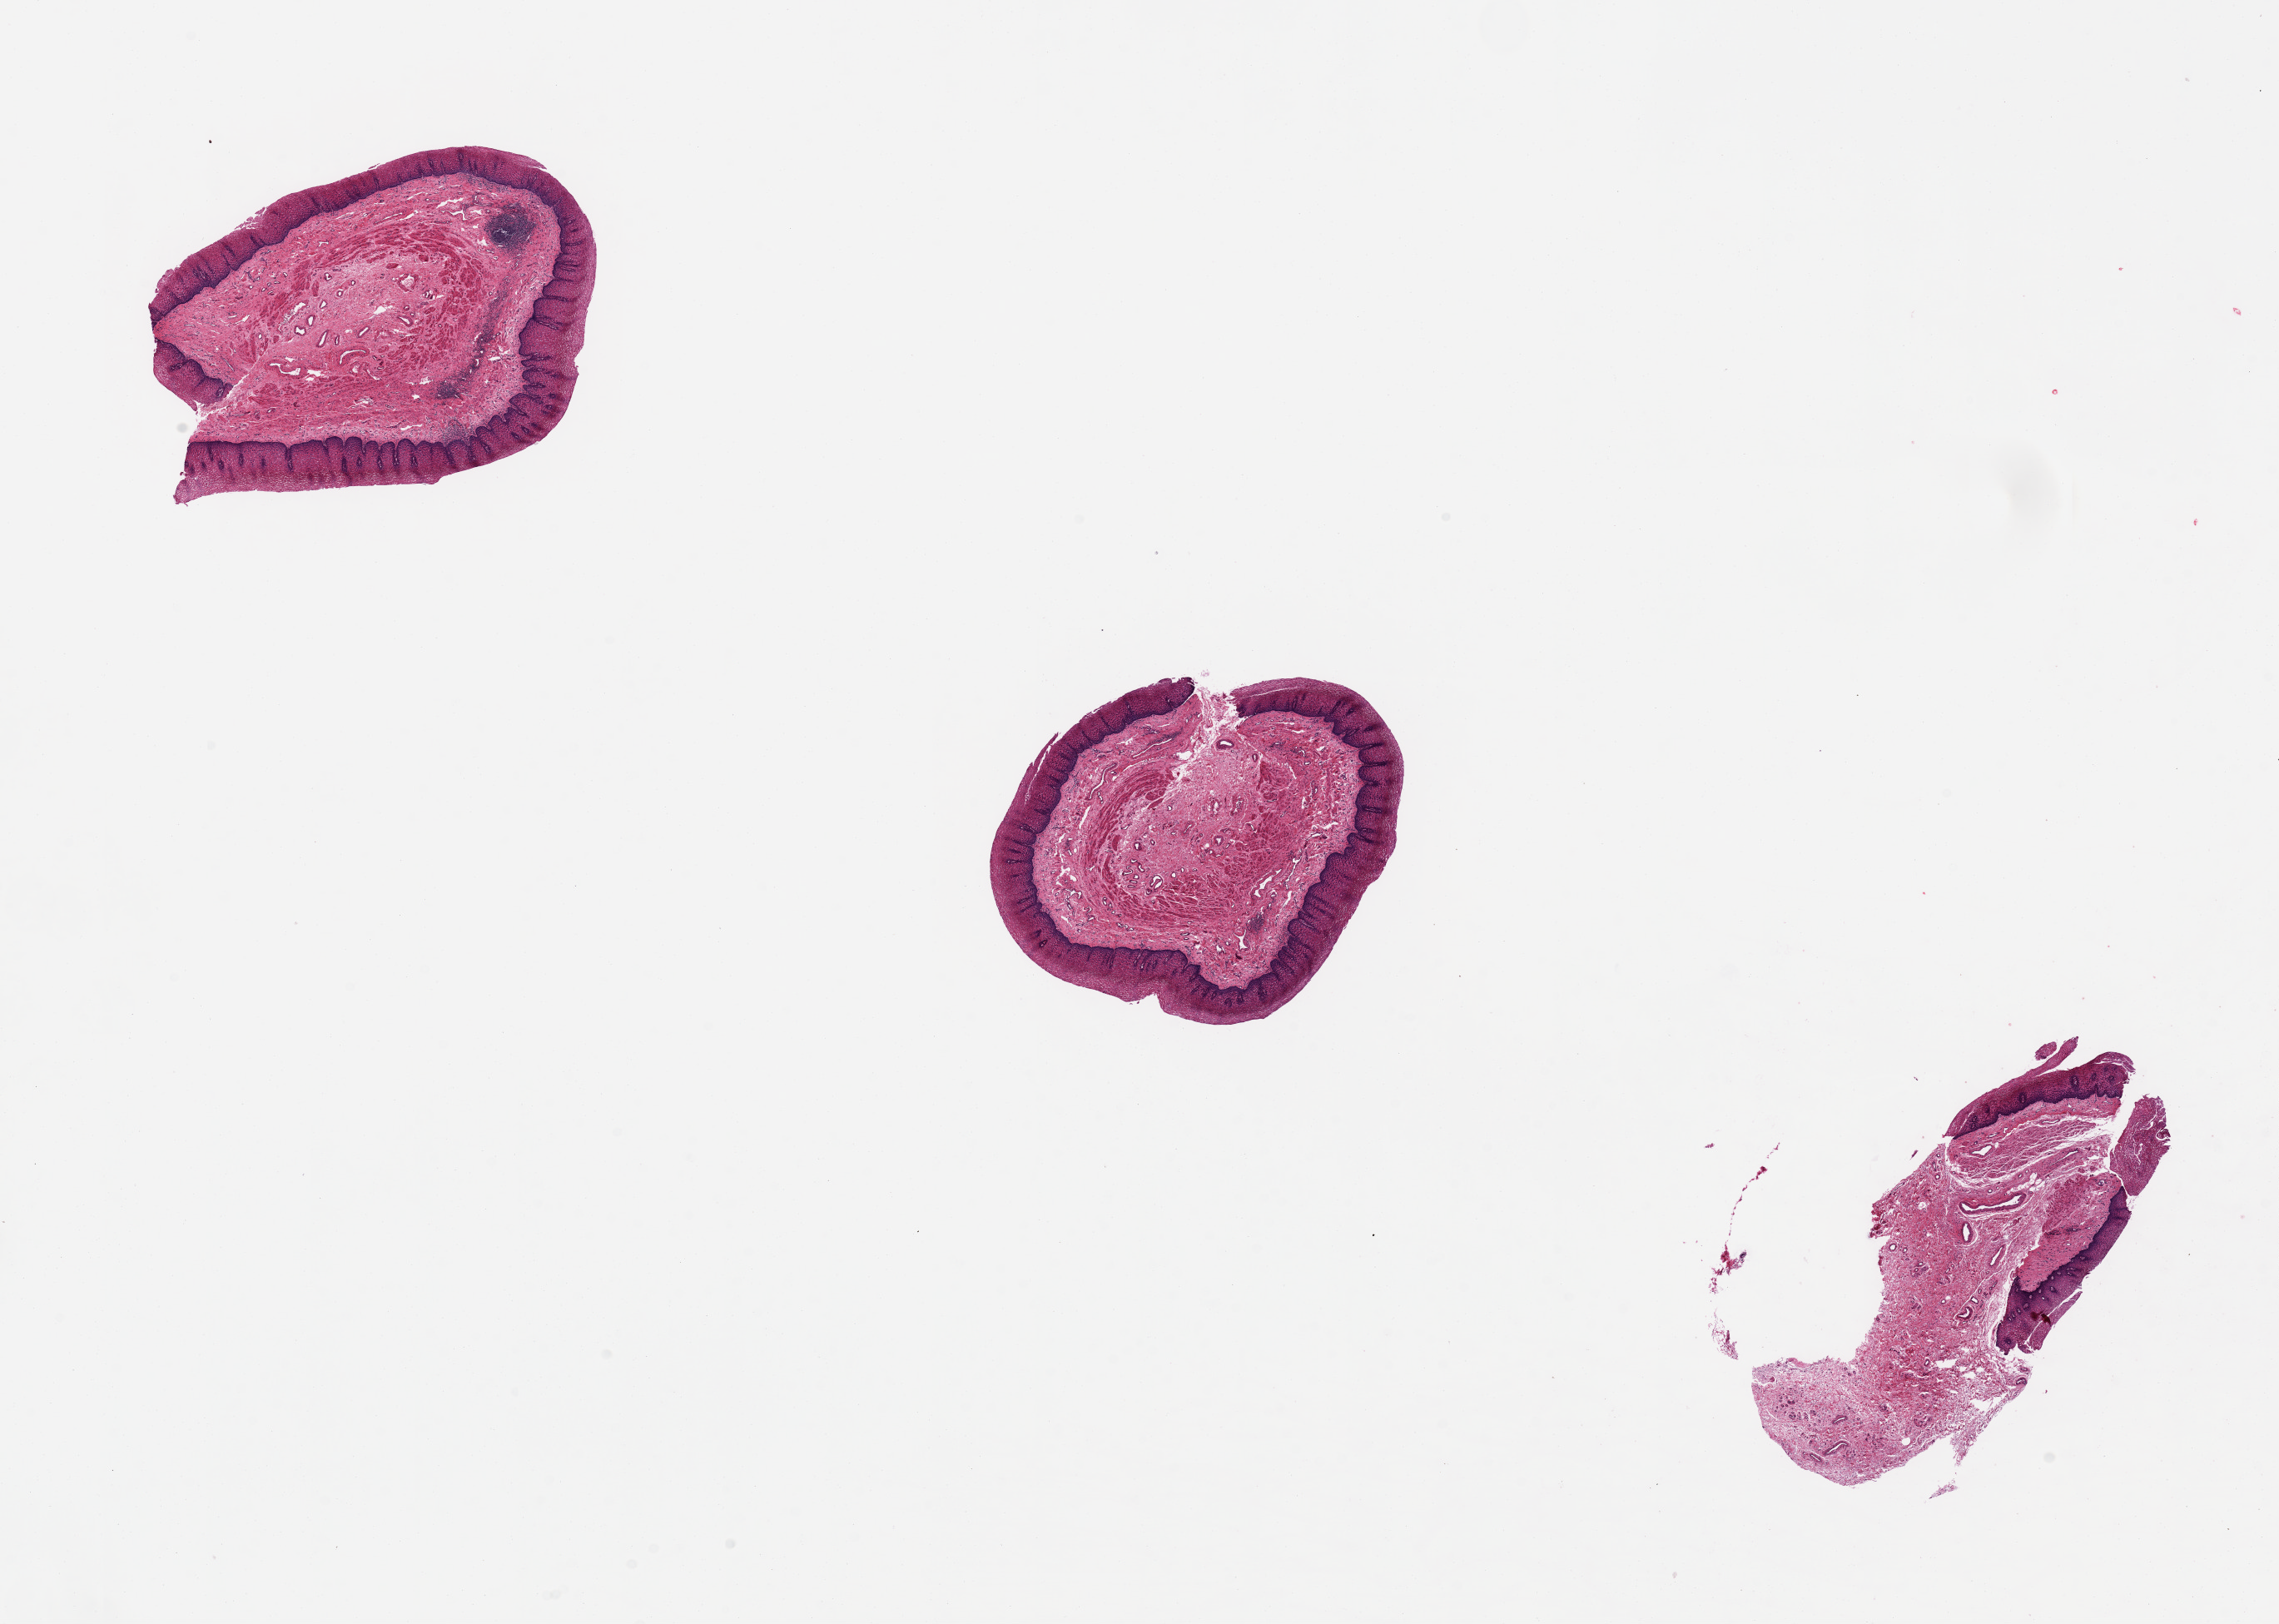
Digitized haematoxylin and eosin-stained section — whole scanned area (about 21.7 x 15.4 mm, slide scanned at 20x) shown as a low-resolution overview; PAXgene-fixed paraffin-embedded (PFPE) section; target tissue: esophageal mucous membrane; tissue donor sample. Donor sex: male.
Reviewer comment on this tissue sample: Mucosa averages 20-25% thickness of specimen thickness0.